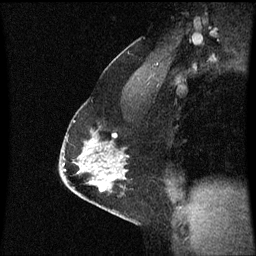
Breast MRI (dynamic contrast-enhanced), one sagittal slice. Position 40 of 60 along the scan axis. Dynamic contrast-enhanced series, image 2 of 3 at this slice position (ordered by acquisition). 1.5 T. TE 4.2 ms, TR 8.9 ms. 256 × 256 image matrix. Female patient, age 47 years. Case-level facts recorded for this patient, not image findings: setting: breast cancer imaged before/during neoadjuvant chemotherapy; receptor status: HR-positive, HER2-negative.
Annotated regions visible in this slice (semi-automatic segmentation, software-assisted and operator-edited):
- analysis volume of interest (the breast-tissue region the enhancement analysis was run in; not a lesion): box from (x=61, y=110) to (x=130, y=209) px
- tumour enhancement mask (voxels above the 70 % enhancement threshold inside the analysis volume of interest): (x=91, y=142)–(x=102, y=191)